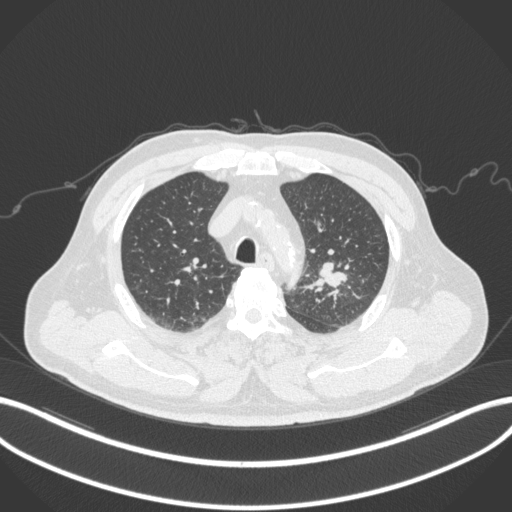
Chest CT, one axial slice; slice 234 of 286 in the series (ordered by position); 120 kVp; lung window (W 1500 / L -600 HU); 1 mm slice thickness; 512 × 512 image matrix, field of view 400 × 400 mm. Male patient, age 67 years. Case-level facts recorded for this patient, not image findings: clinical TNM (as recorded): T2a N1 M0; histopathological grade: G3.
Outlined on this slice (bounding box drawn by a radiologist):
- lung tumour (recorded histology: adenocarcinoma): bounding box (x1, y1, x2, y2) in pixels: (311, 254, 348, 293)